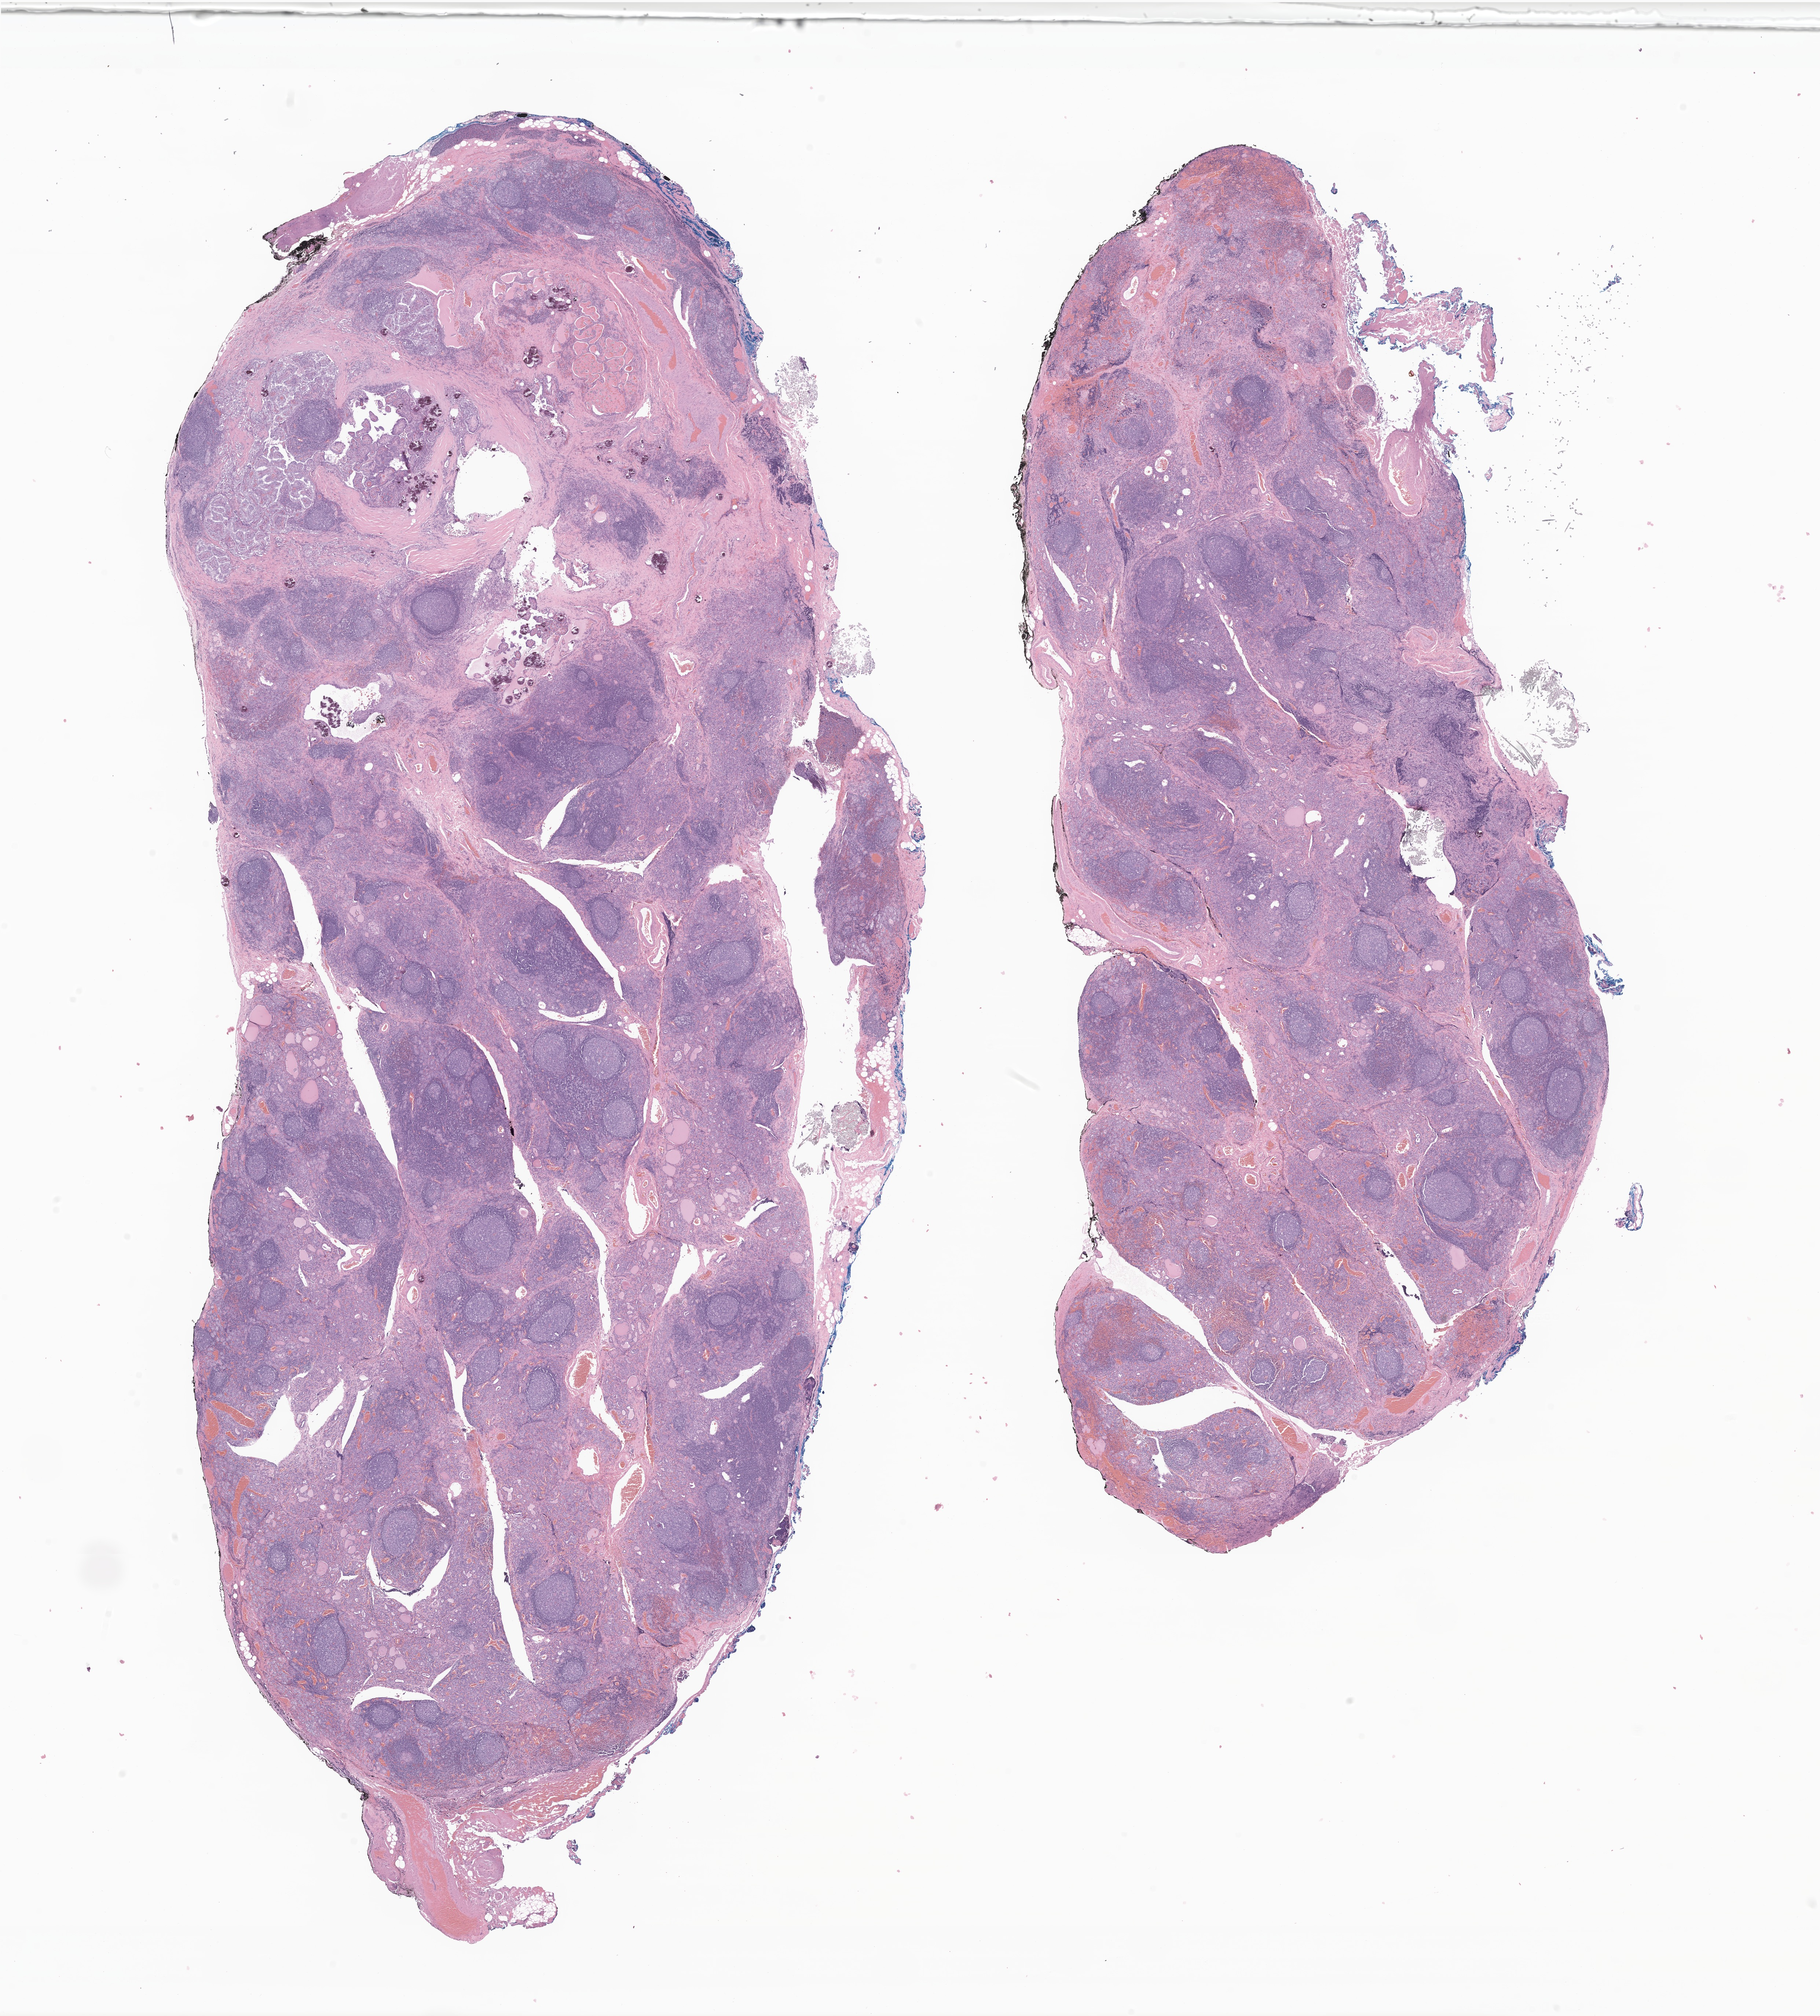
Whole-slide image, hematoxylin and eosin (H&E) stain of tumor tissue from the thyroid, whole scanned area (about 20.9 x 23.2 mm) shown as a low-resolution overview; formalin-fixed, paraffin-embedded (FFPE) tissue. Patient female; age 225 months (18 years 9 months).
* recorded diagnosis: Papillary carcinoma, NOS